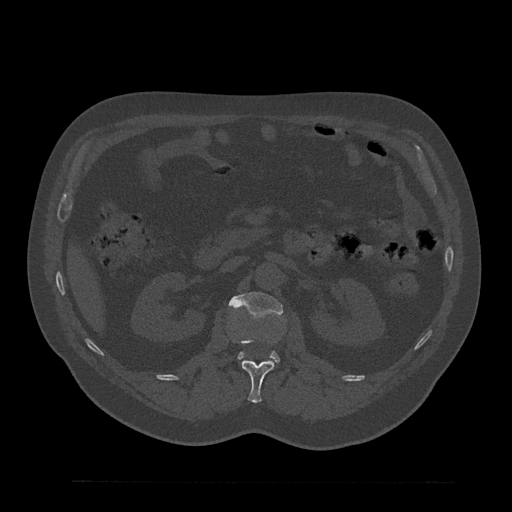
CT including the spine, one axial slice. Reconstruction kernel Br40s/3. Bone window (W 1800 / L 400 HU). 0.5 mm slice thickness. 512 × 512 image matrix. Male patient, age 61 years. From the clinical record (not read from this slice): primary cancer: prostate.
Annotated regions visible in this slice (semi-automatically segmented with operator editing):
- L1 vertebra: bounding box [x1, y1, x2, y2] px = [231, 336, 275, 403]
- L2 vertebra: [228, 292, 283, 362]